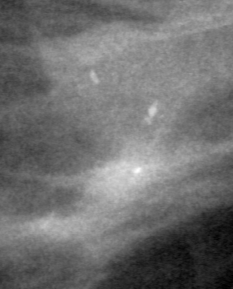
Region of interest cut from a scanned film mammogram (one marked finding), right breast, MLO view.
Marked abnormality: calcifications, morphology pleomorphic, distribution clustered; BI-RADS assessment category 4; pathology (as recorded): malignant.